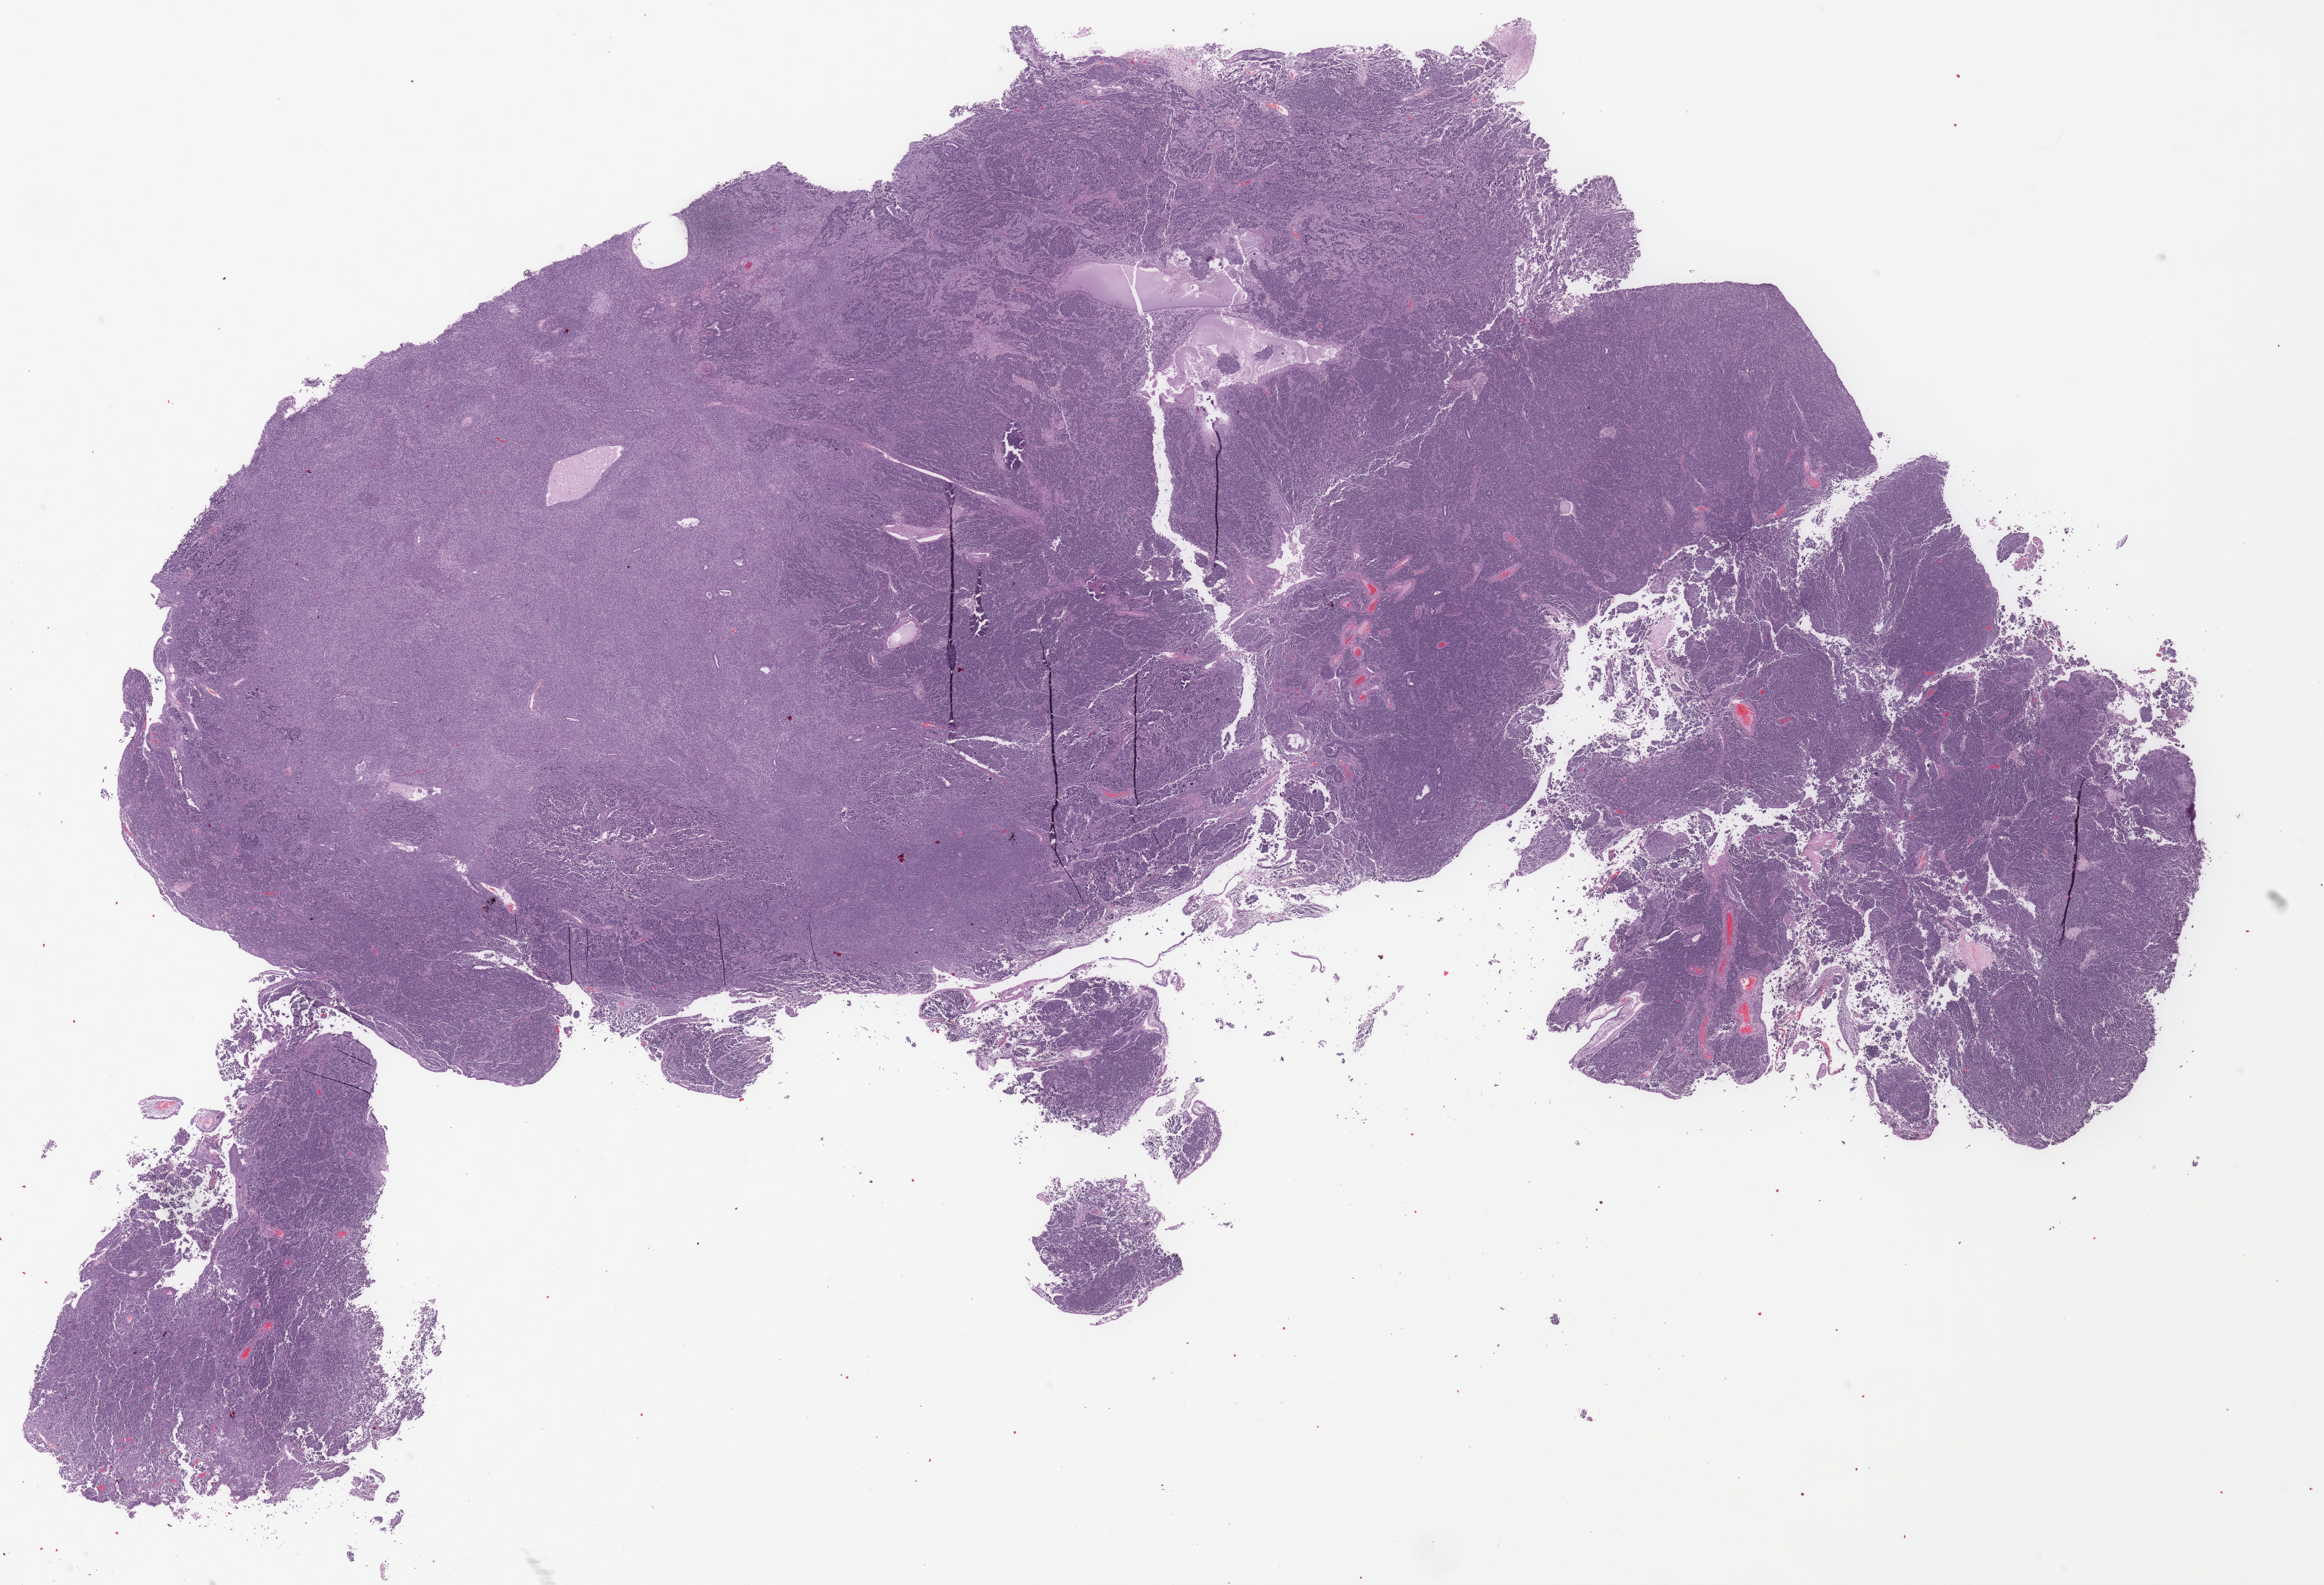
Whole-slide histology image, H&E, whole scanned area (about 25.4 x 17.3 mm) shown as a low-resolution overview. Formalin-fixed paraffin-embedded (FFPE) diagnostic section. Sample: primary tumour, uterus. Female, age 71 years at initial diagnosis.
FIGO stage: IVB. Diagnosis: Mullerian mixed tumor (endometrium).